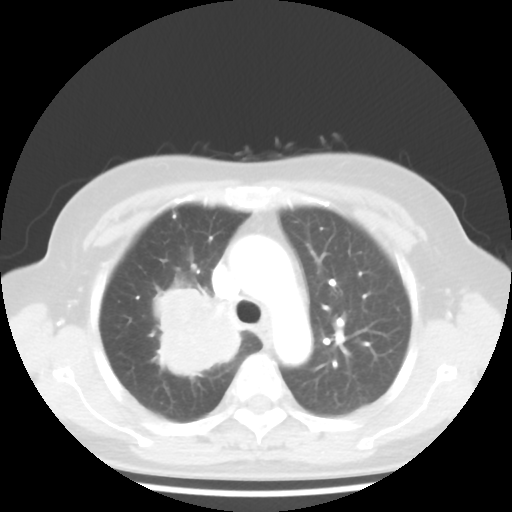
Chest CT, one axial slice; position 31 of 44 along the scan axis; reconstruction kernel STANDARD; 100 kVp; lung window (W 1500 / L -600 HU); 5 mm slice thickness; 512 × 512 image matrix, field of view 316 × 316 mm. Patient: female, 62 years. From the clinical record (not read from this slice): clinical TNM (as recorded): T3 N0 M0.
Outlined on this slice (bounding box drawn by a radiologist):
- lung tumour (recorded histology: small cell carcinoma): box from (x=137, y=284) to (x=251, y=383) px